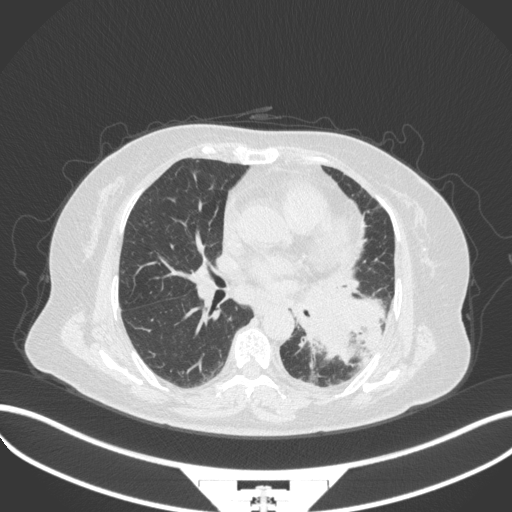
Chest CT, one axial slice; reconstruction kernel B31f; 120 kVp; lung window (W 1500 / L -600 HU); 1 mm slice thickness; 512 × 512 image matrix, field of view 400 × 400 mm. Female patient, age 69 years. From the clinical record (not read from this slice): clinical TNM (as recorded): T2b N3 M1.
Structures marked on this image (bounding box drawn by a radiologist):
- lung tumour (recorded histology: adenocarcinoma): bounding box <298,286,390,366> (left, top, right, bottom; pixels)